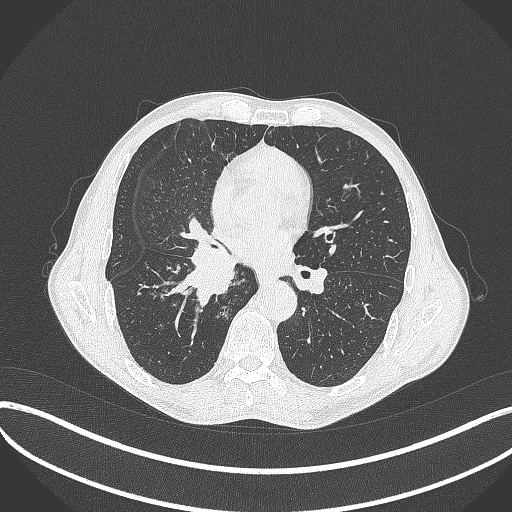
Chest CT, one axial slice. Slice 217 of 481 in the series (ordered by position). Lung window (W 1500 / L -600 HU). 1 mm slice thickness. 512 × 512 image matrix, field of view 400 × 400 mm. Patient: male, 65 years. Case-level facts recorded for this patient, not image findings: clinical TNM (as recorded): T2a N0 M0; histopathological grade: G2.
Annotated regions visible in this slice (rectangle marked by the reading radiologist):
- lung tumour (recorded histology: squamous cell carcinoma): bounding box <165,239,247,312> (left, top, right, bottom; pixels)